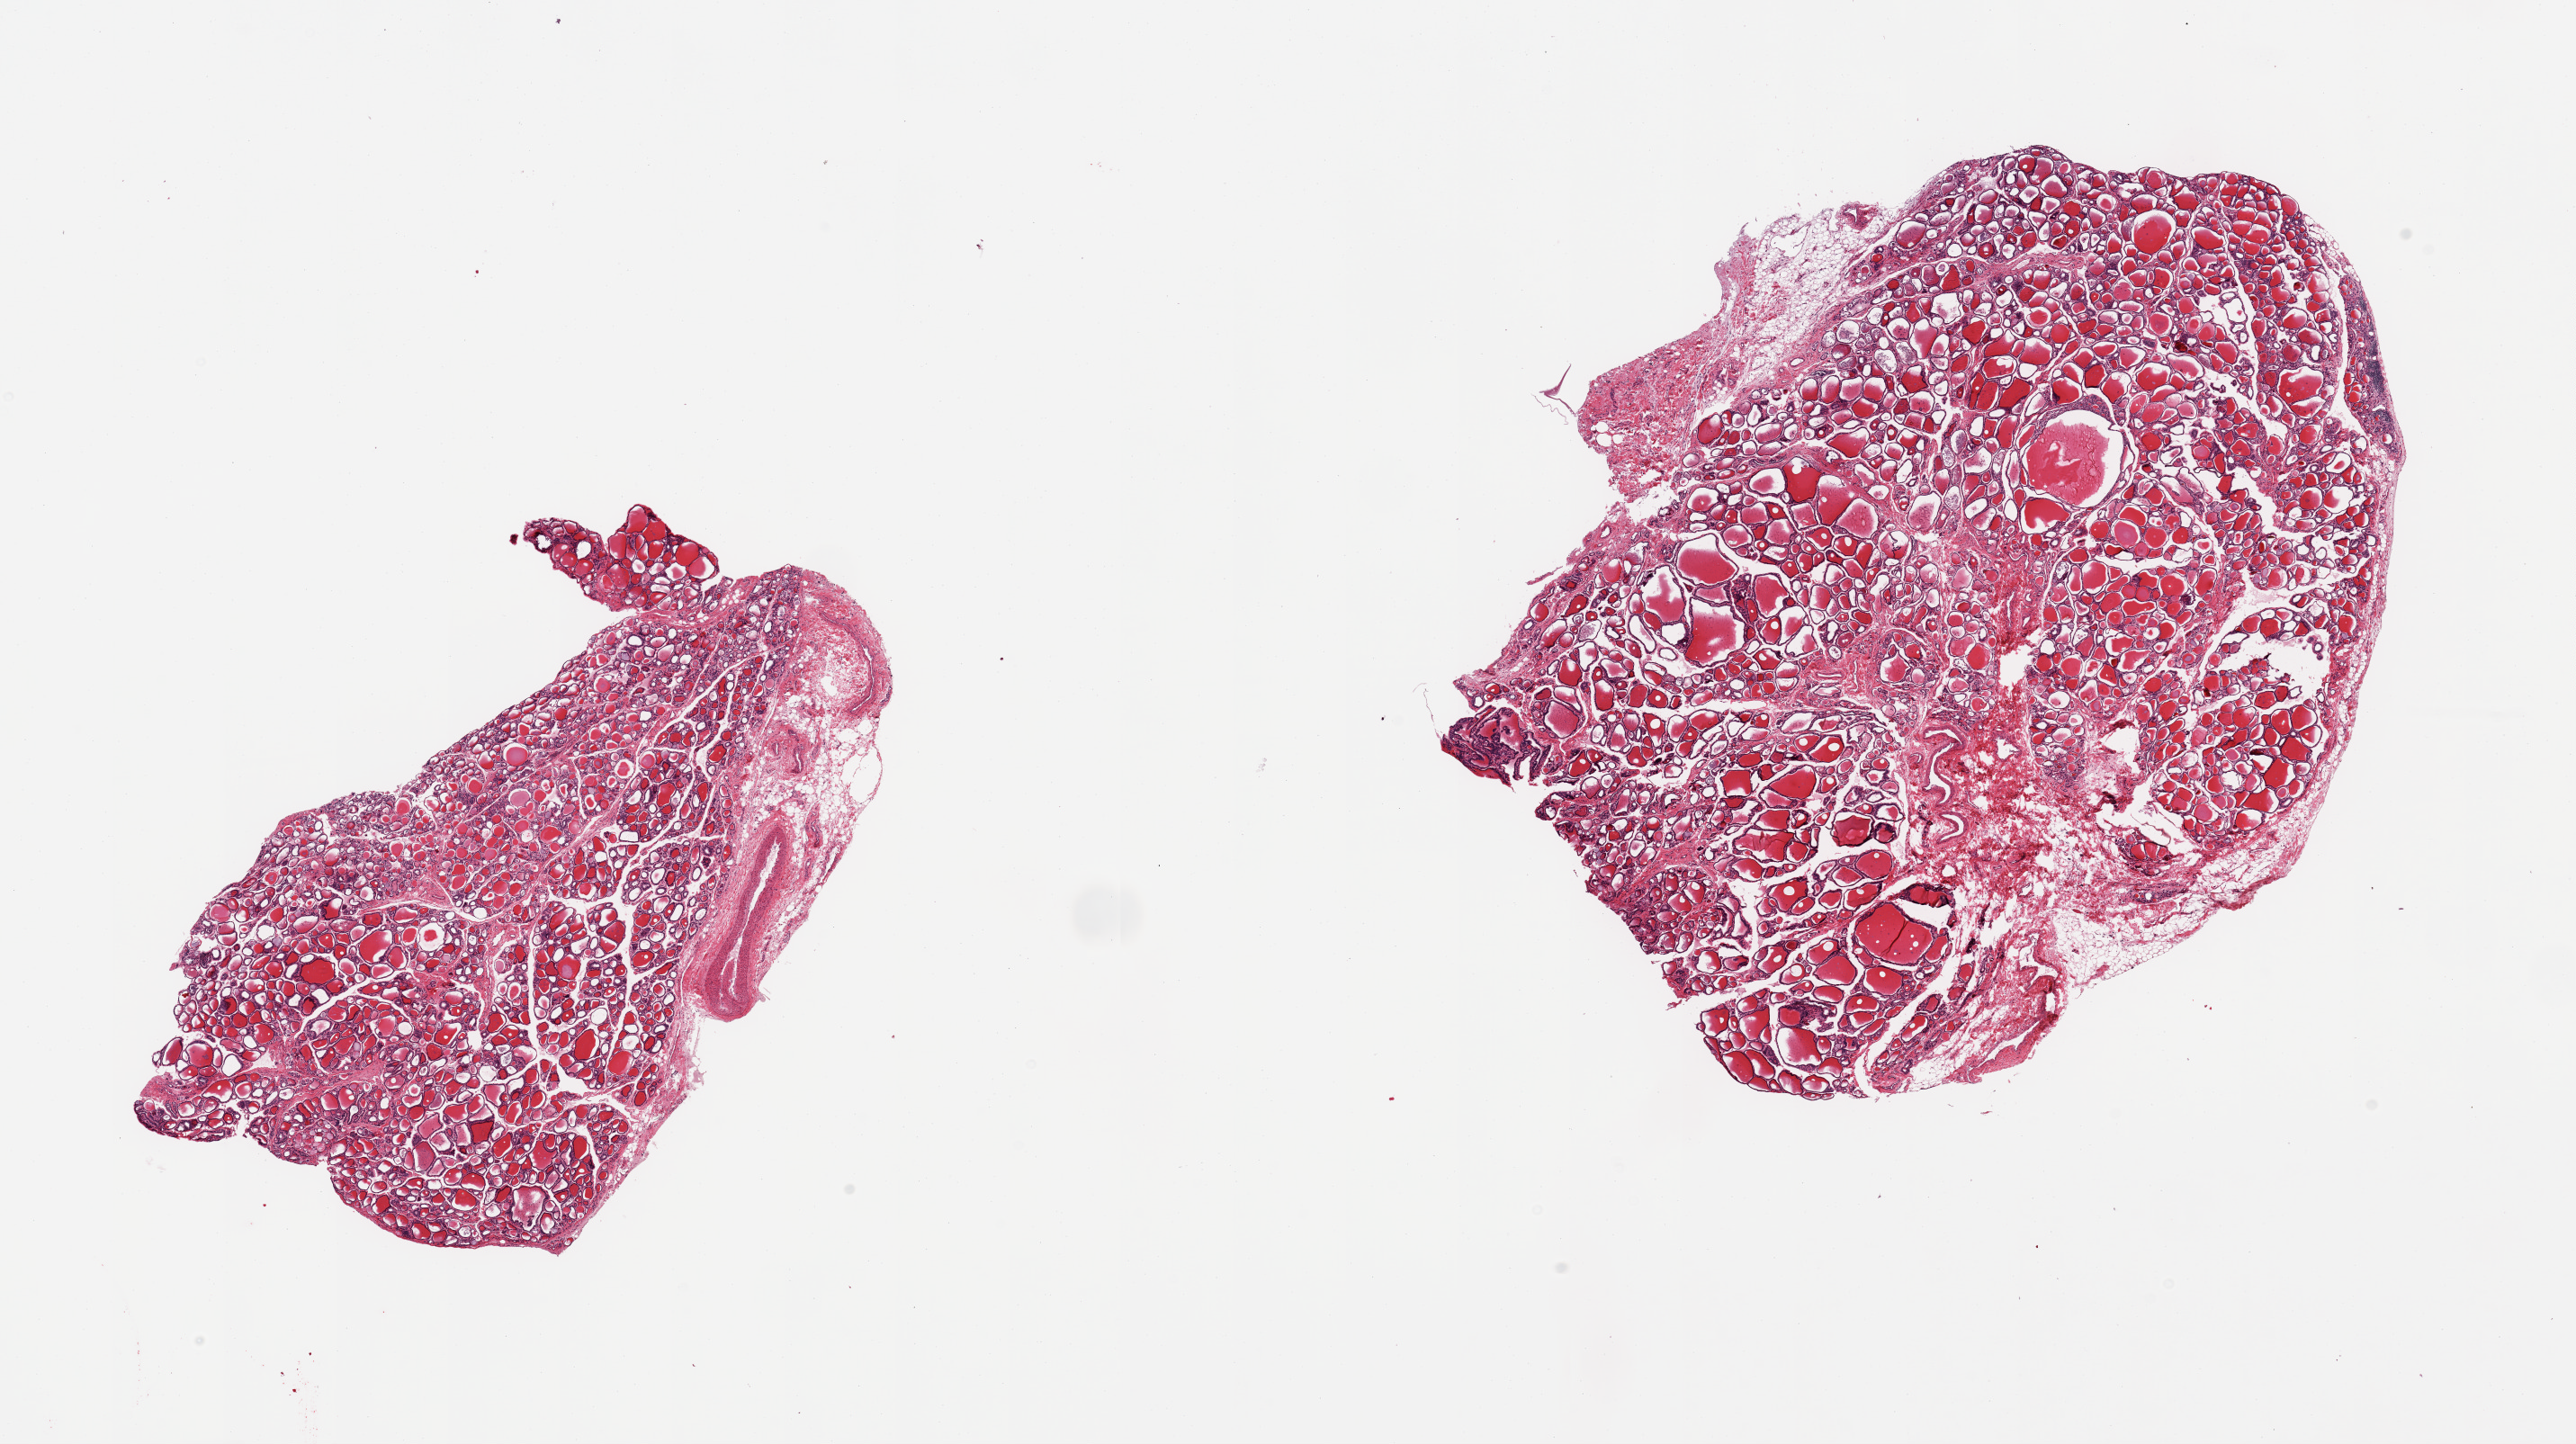
Digitized haematoxylin and eosin-stained section, brightfield, low-resolution overview of the scanned area, about 22.6 x 12.7 mm. PAXgene-fixed paraffin-embedded (PFPE) section. Target tissue: thyroid. Tissue donor sample.
• review note (as recorded): 2 pieces, no abnormalities, trace adherent fat